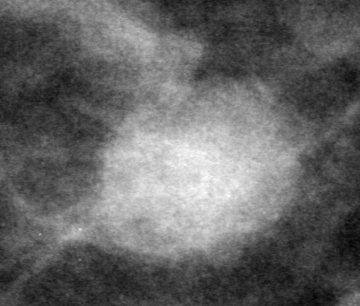
Region of interest cut from a scanned film mammogram (one marked finding), right breast, CC view, BI-RADS breast density category 2 (scale 1–4).
Finding: mass, shape oval, margins ill defined; BI-RADS assessment category 0 (incomplete: needs additional imaging); pathology result (as recorded, not read from the image): benign.